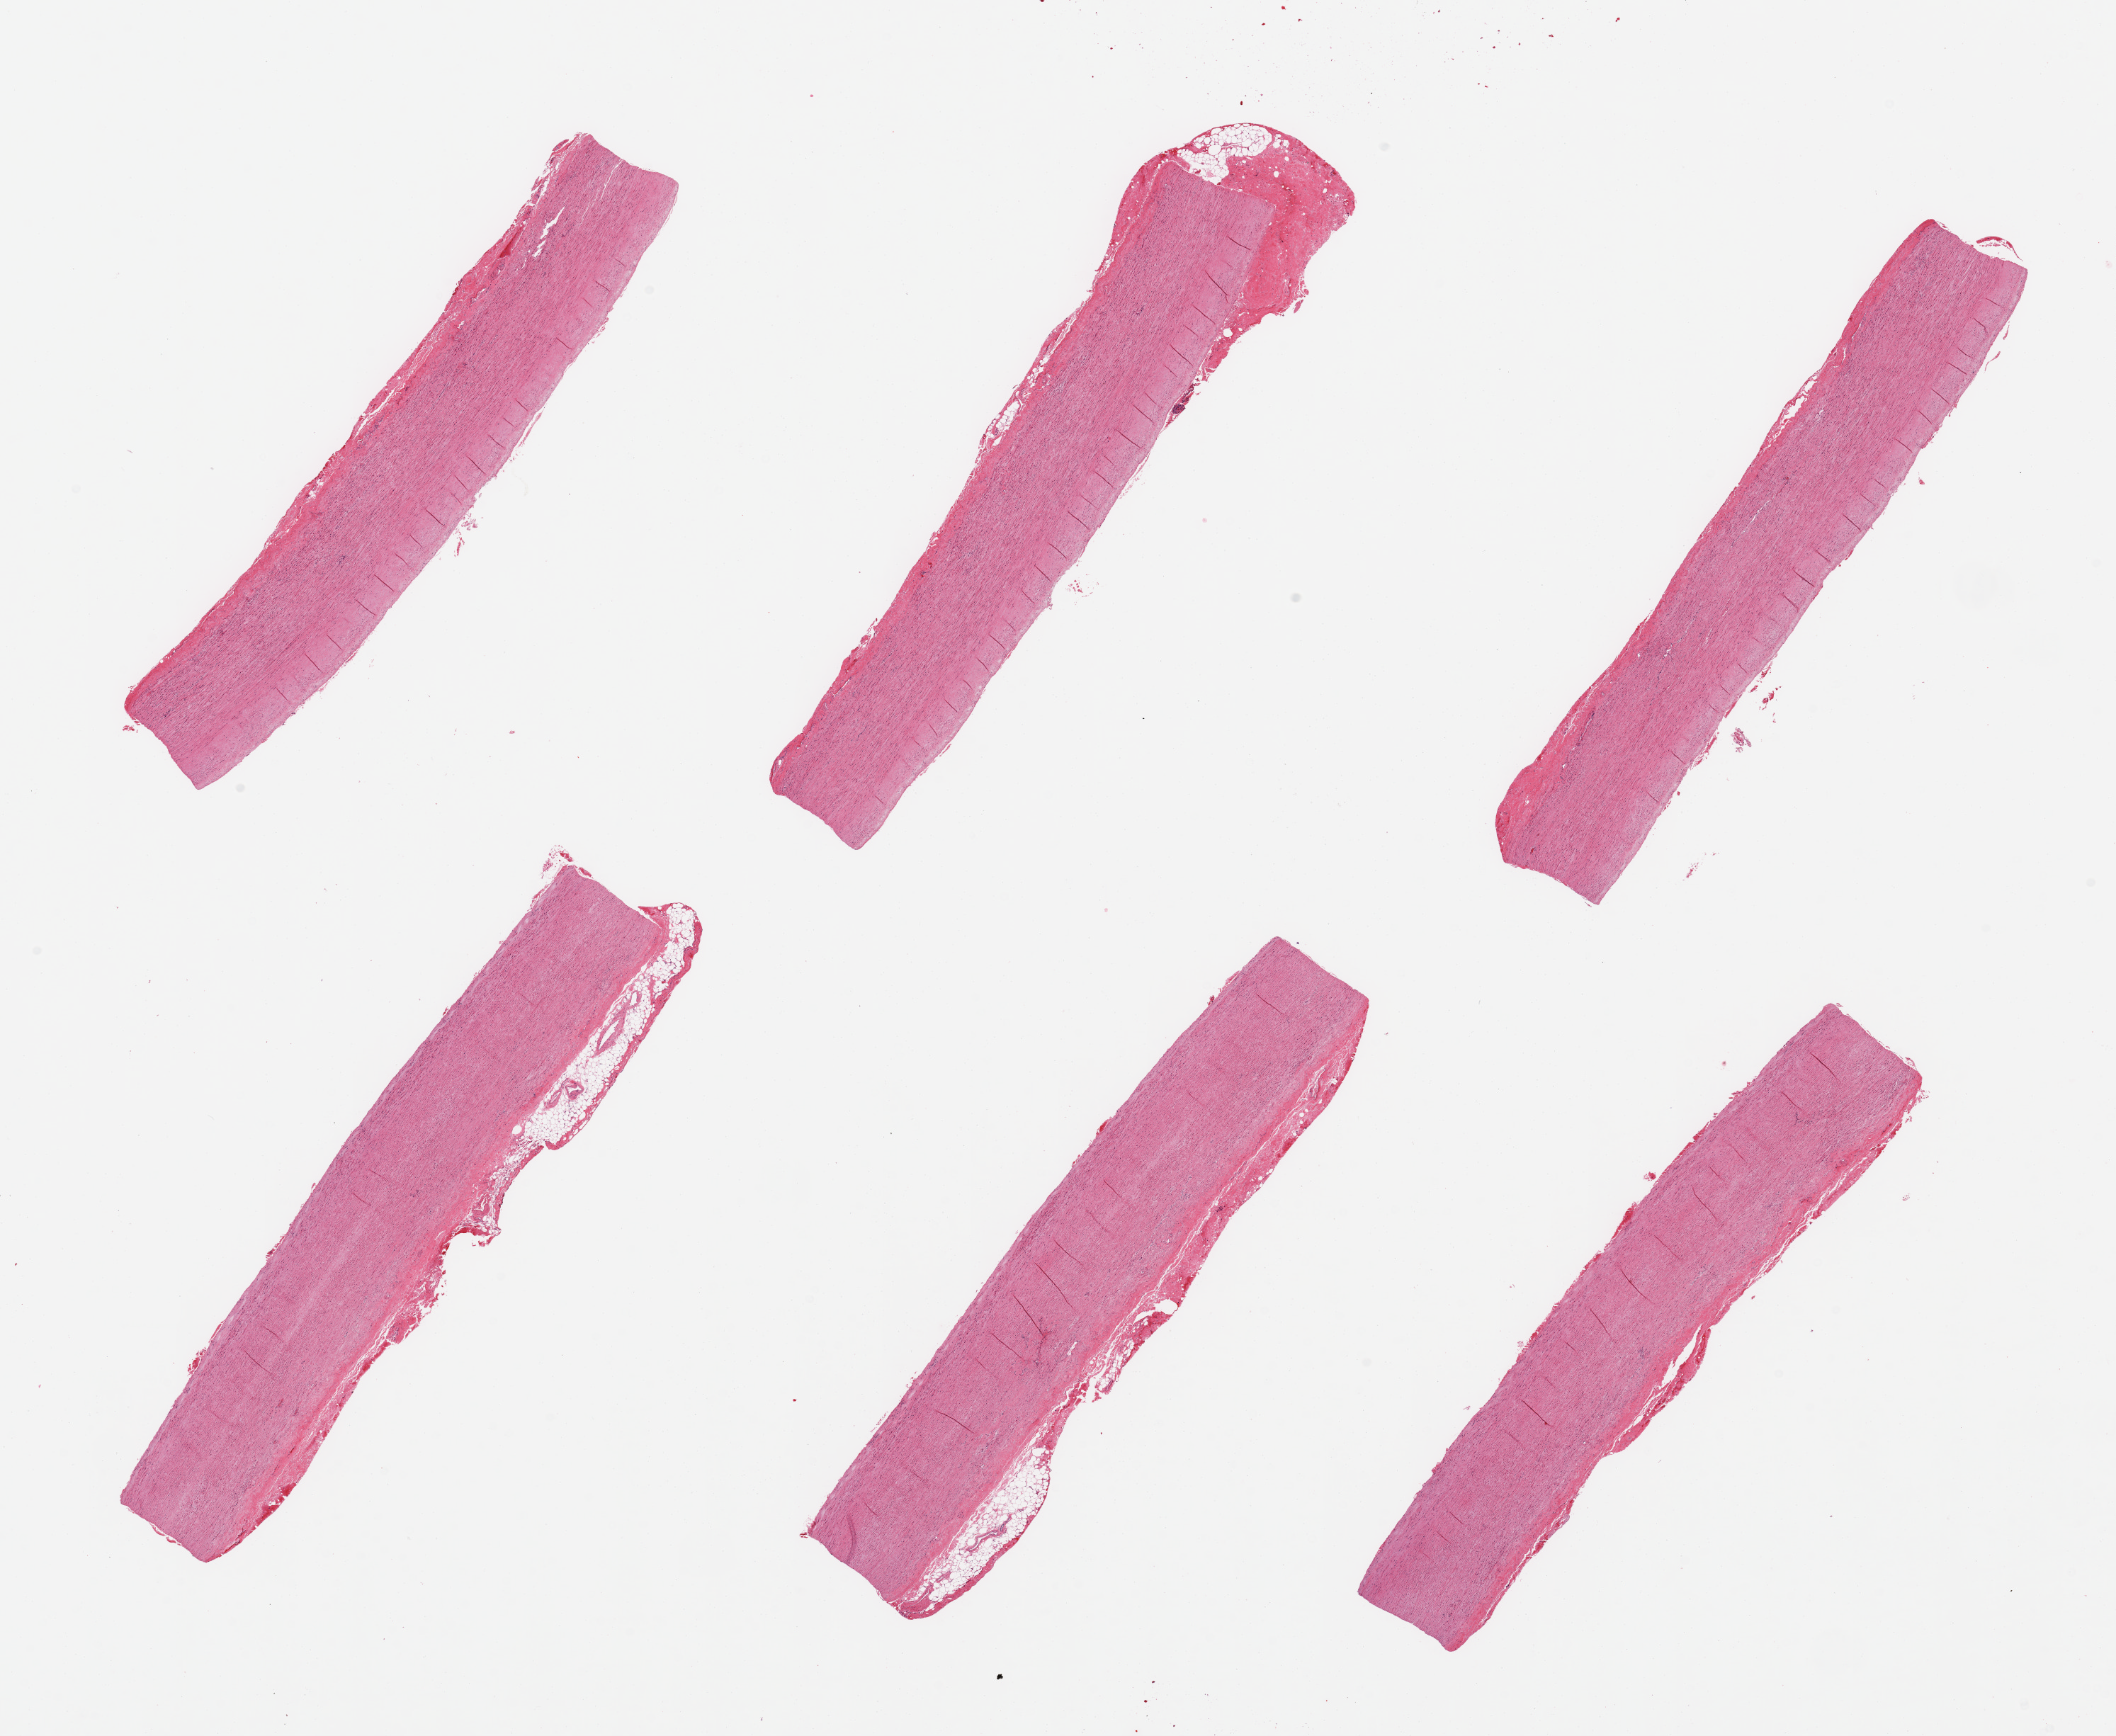
Whole-slide image, H&E stain, whole scanned area (about 23.6 x 19.4 mm, slide scanned at 20x) shown as a low-resolution overview. PAXgene-fixed, paraffin-embedded tissue. Section of aorta (target tissue). Tissue donor sample. Male donor.
Reviewer comment on this tissue sample: 6 pieces; minimal intimal fibrous thickening; well trimmed.